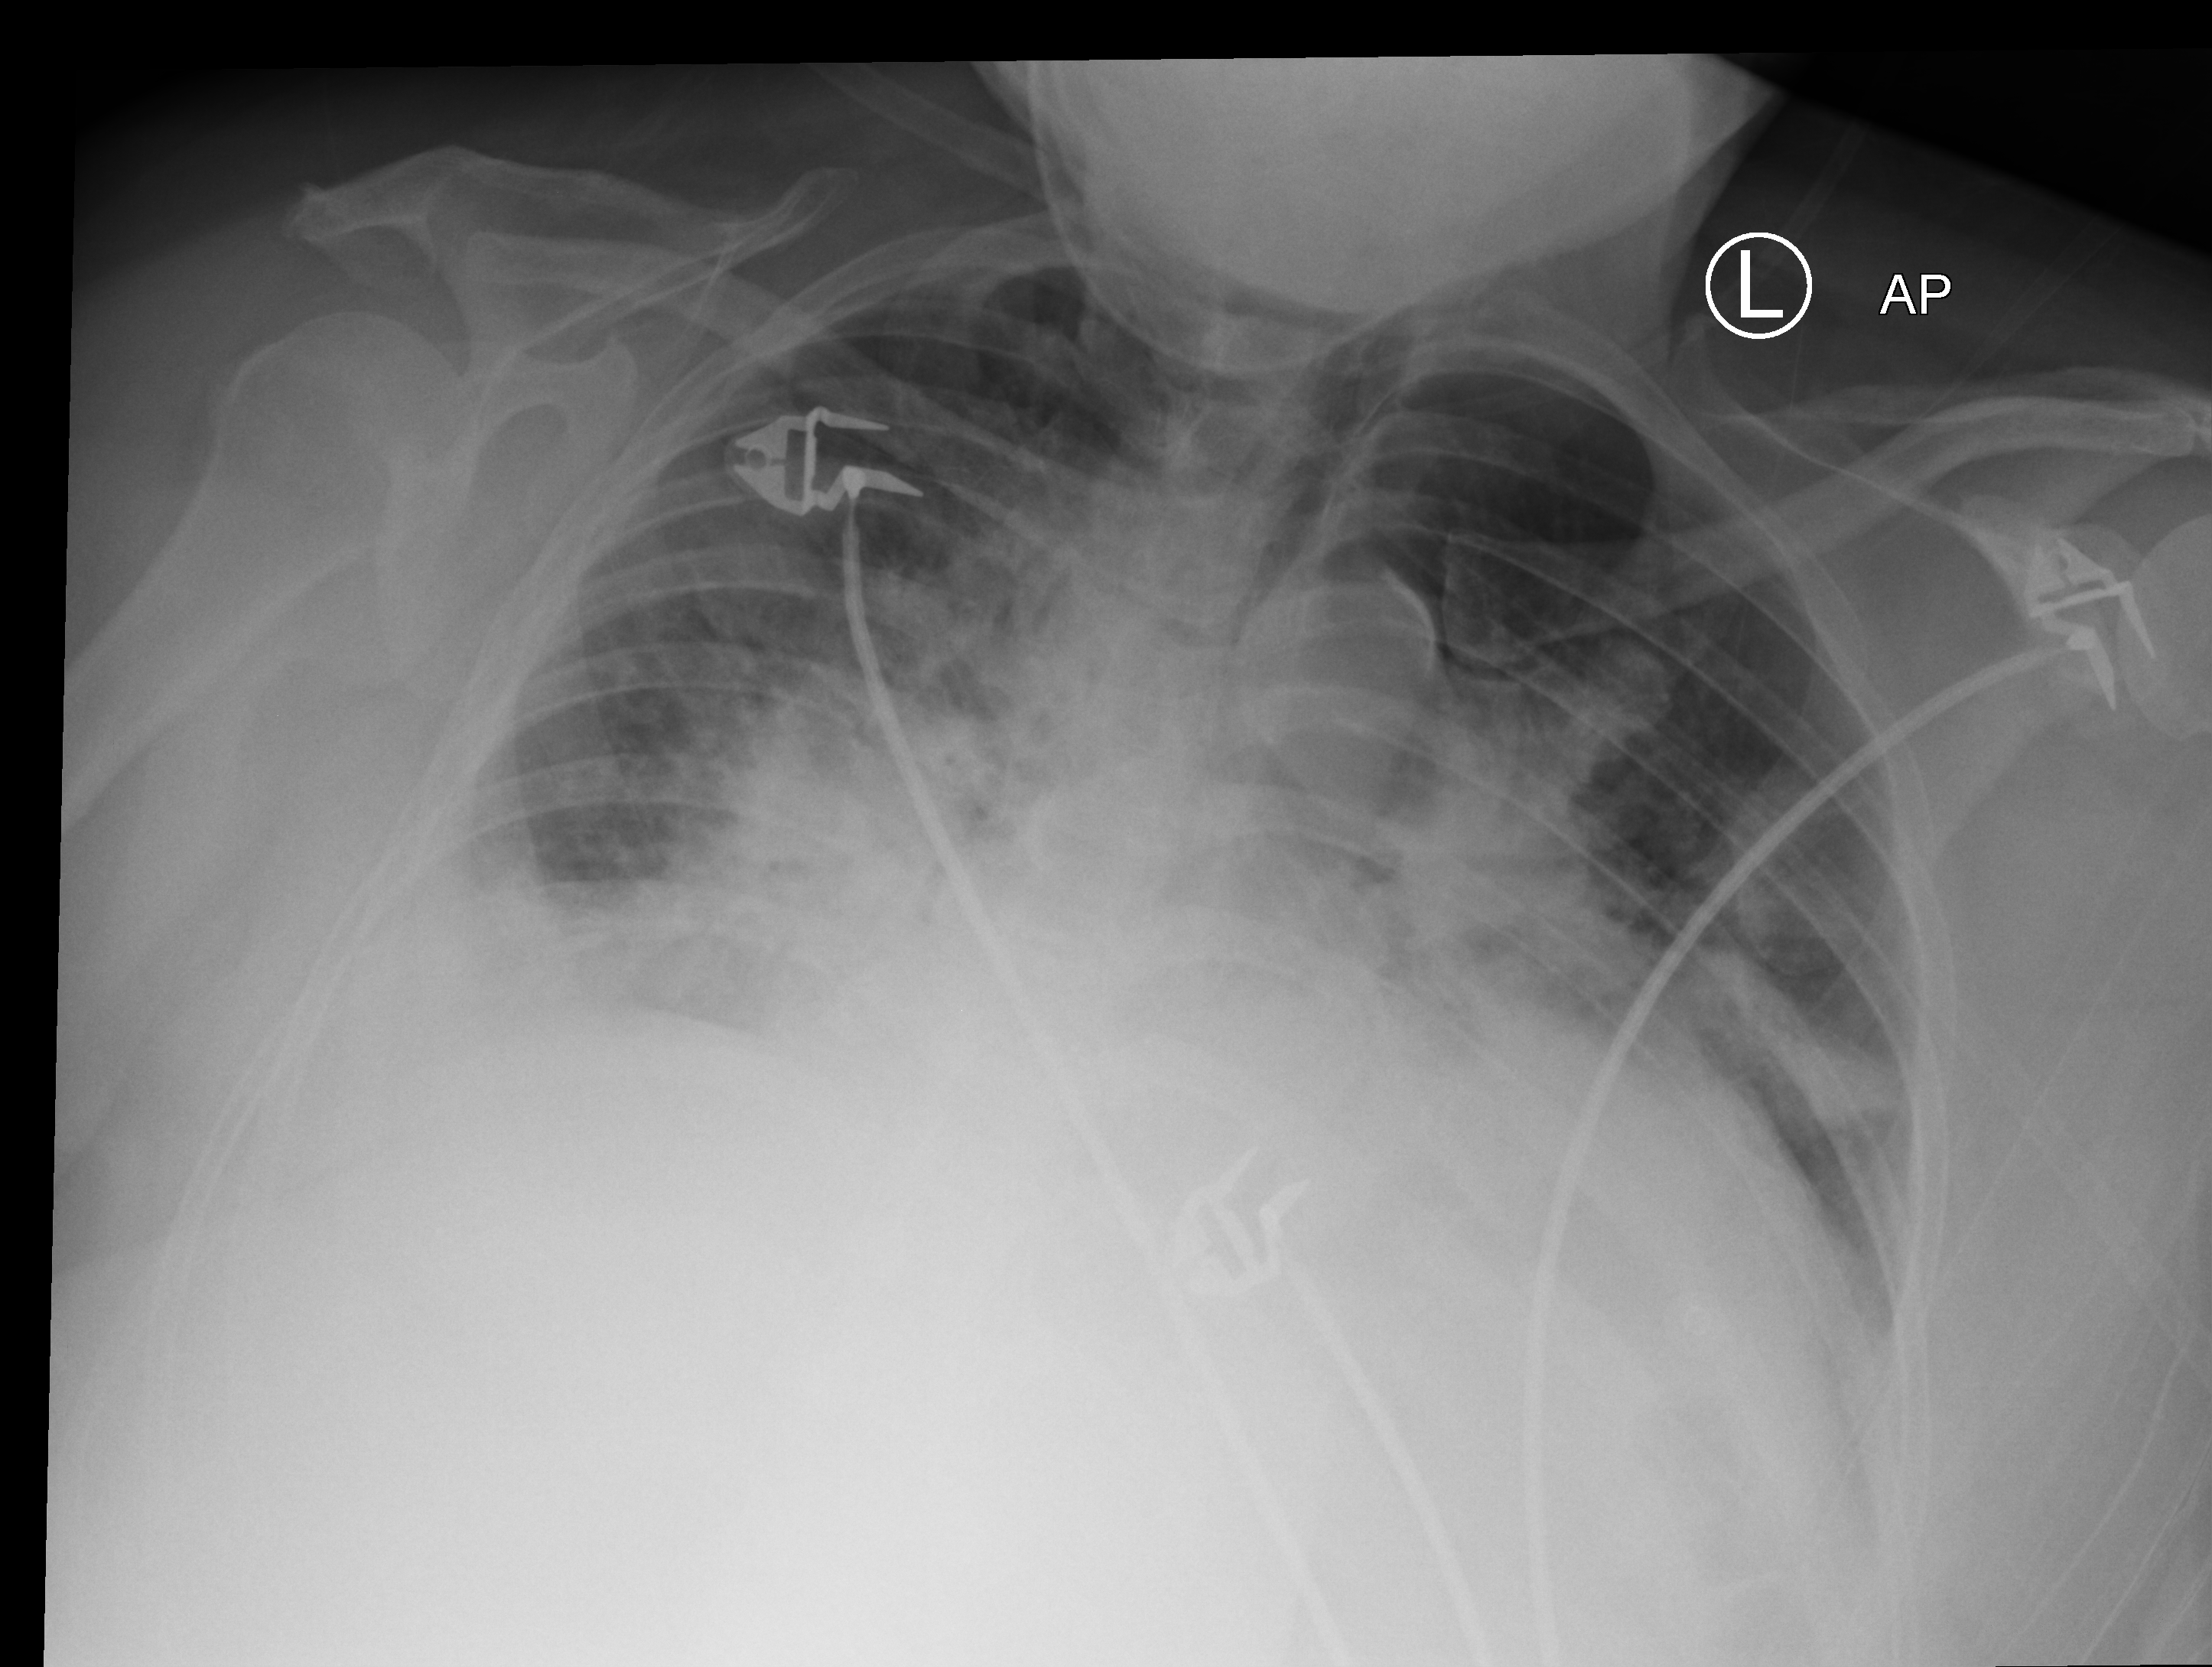
Chest X-ray (portable); anteroposterior (AP) projection. Patient hospitalised with COVID-19; female, aged 18–59 years.
From the hospital-stay record, not from the radiograph (when in the stay this image was taken is not recorded): mechanically ventilated during this hospital stay: no.